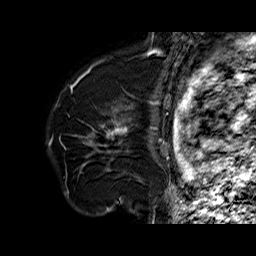
Breast MRI (dynamic contrast-enhanced), one sagittal slice. Dynamic contrast-enhanced series, time point 2 of 6 at this slice position (early post-contrast). 1.5 T. TE 6.4 ms, TR 32.7 ms. 4 mm slice thickness. 256 × 256 image matrix, field of view 200 × 200 mm. Female patient. Case-level facts recorded for this patient, not image findings: setting: breast cancer imaged before/during neoadjuvant chemotherapy; receptor status: HR-positive, HER2-negative.
Annotated regions visible in this slice (semi-automatically segmented with operator editing):
- analysis volume of interest (the breast-tissue region the enhancement analysis was run in; not a lesion): bounding box <79,110,135,178> (left, top, right, bottom; pixels)
- tumour enhancement mask (voxels above the 100 % enhancement threshold inside the analysis volume of interest): <94,122,128,136>